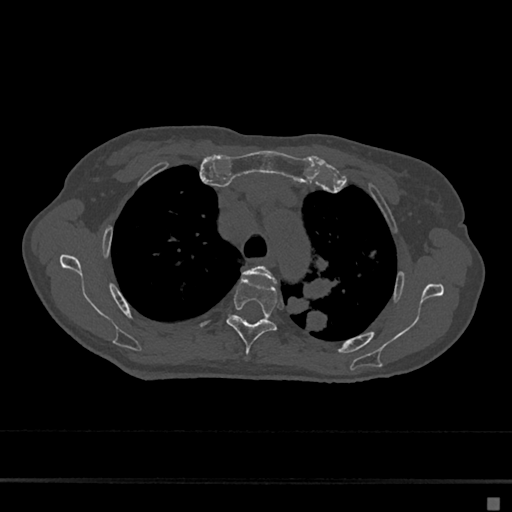
CT including the spine, one axial slice. Slice 501 of 797 in the series (ordered by position). Reconstruction kernel Br40s/3. Bone window (W 1800 / L 400 HU). 0.5 mm slice thickness. 512 × 512 image matrix. Female patient, age 68 years. Case-level facts recorded for this patient, not image findings: primary cancer: renal.
Outlined on this slice (semi-automatically segmented with operator editing):
- T3 vertebra: bounding box [x1, y1, x2, y2] px = [243, 265, 275, 282]
- T4 vertebra: [226, 279, 278, 355]